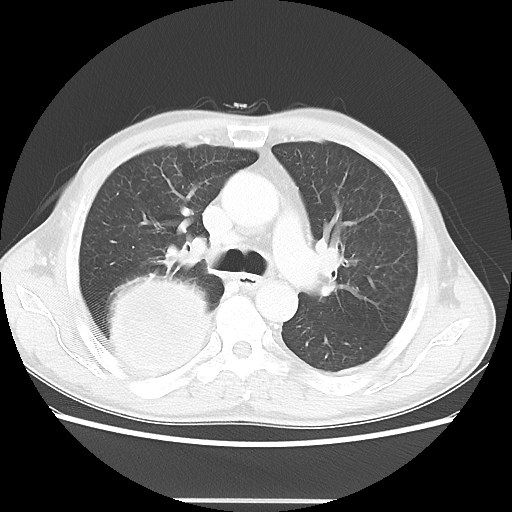
Chest CT, one axial slice. Slice 32 of 48 in the series (ordered by position). Reconstruction kernel LUNG. 100 kVp. Lung window (W 1500 / L -600 HU). 5 mm slice thickness. 512 × 512 image matrix. Patient: male, 66 years. From the clinical record (not read from this slice): clinical TNM (as recorded): T4 N1 M1; histopathological grade: G3.
Annotated regions visible in this slice (bounding box drawn by a radiologist):
- lung tumour (recorded histology: small cell carcinoma): bounding box <97,272,222,389> (left, top, right, bottom; pixels)